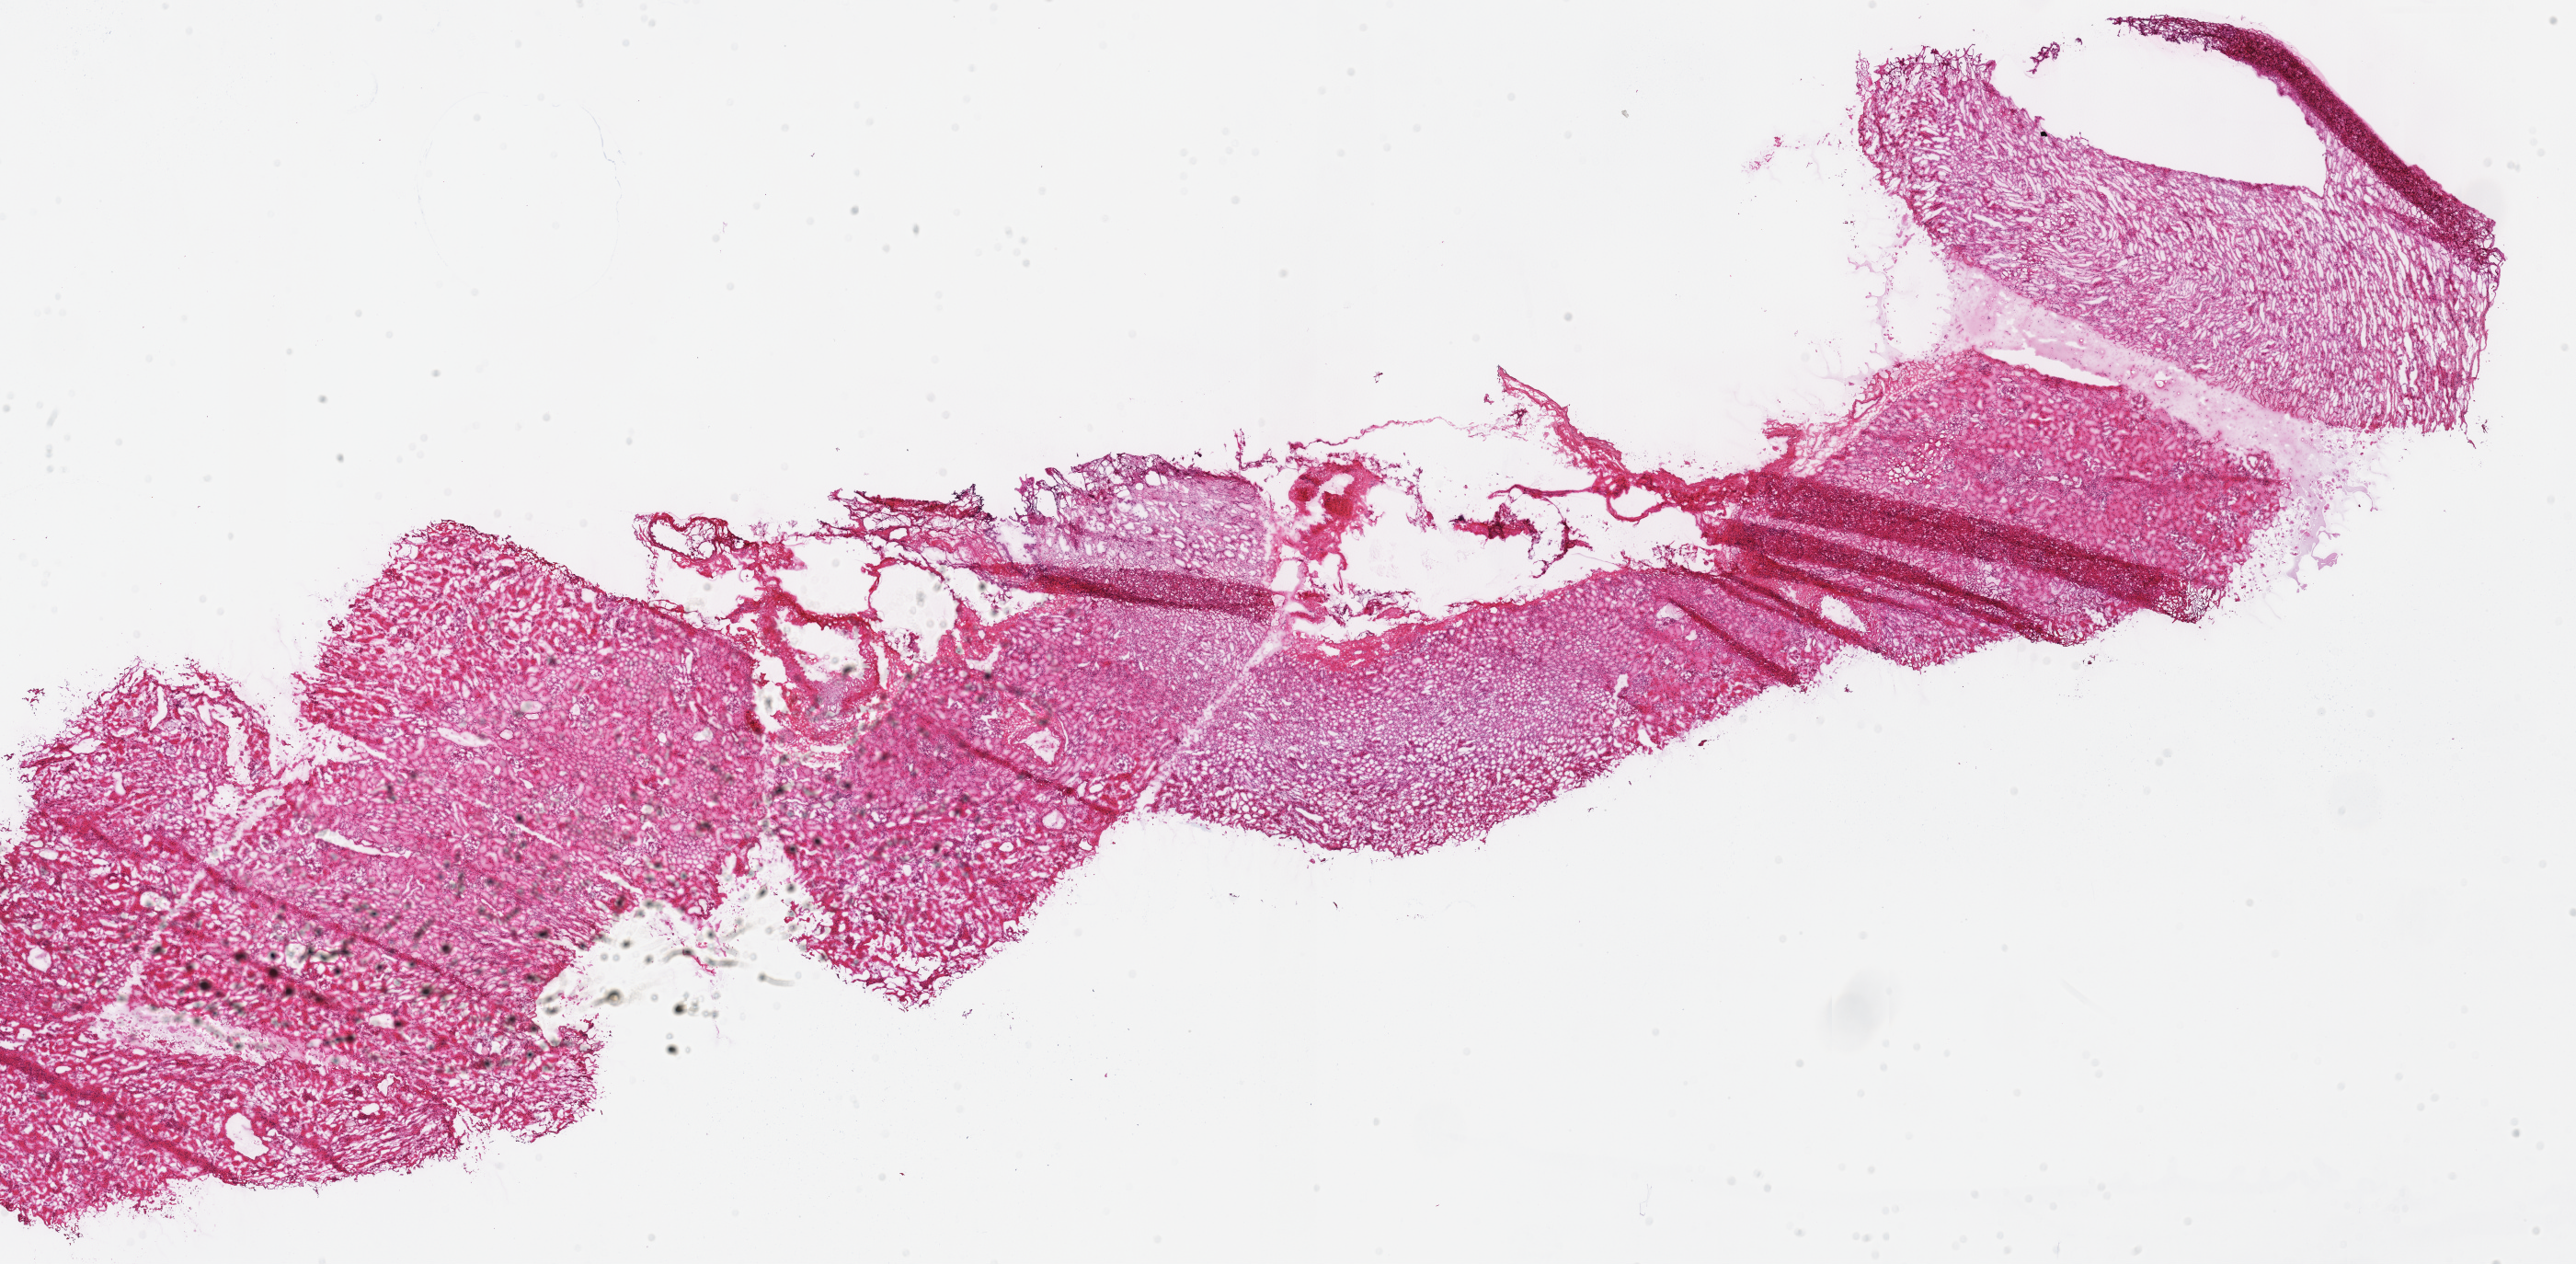
Whole-slide histology image, H&E-stained — a low-resolution overview of the entire scanned area, about 22.0 x 10.8 mm (acquisition: 40x scan), frozen section from the top of the tissue portion, solid tissue normal (non-tumour tissue) sample from the kidney. Female, age 44 years at initial diagnosis.
This section: solid tissue normal (non-tumour) sample from the same patient. Patient diagnosis: Renal cell carcinoma, chromophobe type.